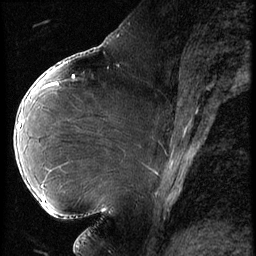
Breast MRI (dynamic contrast-enhanced), one sagittal slice; position 27 of 62 along the scan axis; 3 images stored at this slice position (order not interpretable as contrast timing); 1.5 T; TE 4.2 ms, TR 9 ms; 2.5 mm slice thickness; 256 × 256 image matrix. Female patient, age 43 years. Case-level facts recorded for this patient, not image findings: setting: breast cancer imaged before/during neoadjuvant chemotherapy; receptor status: HER2-positive.
Structures marked on this image (semi-automatically segmented with operator editing):
- analysis volume of interest (the breast-tissue region the enhancement analysis was run in; not a lesion): bounding box <15,90,82,203> (left, top, right, bottom; pixels)
- tumour enhancement mask (voxels above the 140 % enhancement threshold inside the analysis volume of interest): <18,124,21,128>